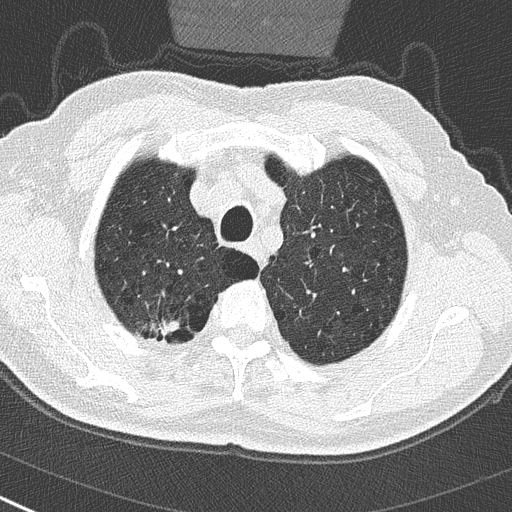
Low-dose screening chest CT, one axial slice. Slice 242 of 290 in the series (ordered by position). Reconstruction kernel B50f. 120 kVp. Lung window (W 1500 / L -600 HU). 512 × 512 image matrix, field of view 300 × 300 mm.
Annotated regions visible in this slice (outlined manually by an expert reader):
- lesion 1 (tumor, upper lobe of right lung): bounding box <150,318,180,339> (left, top, right, bottom; pixels)